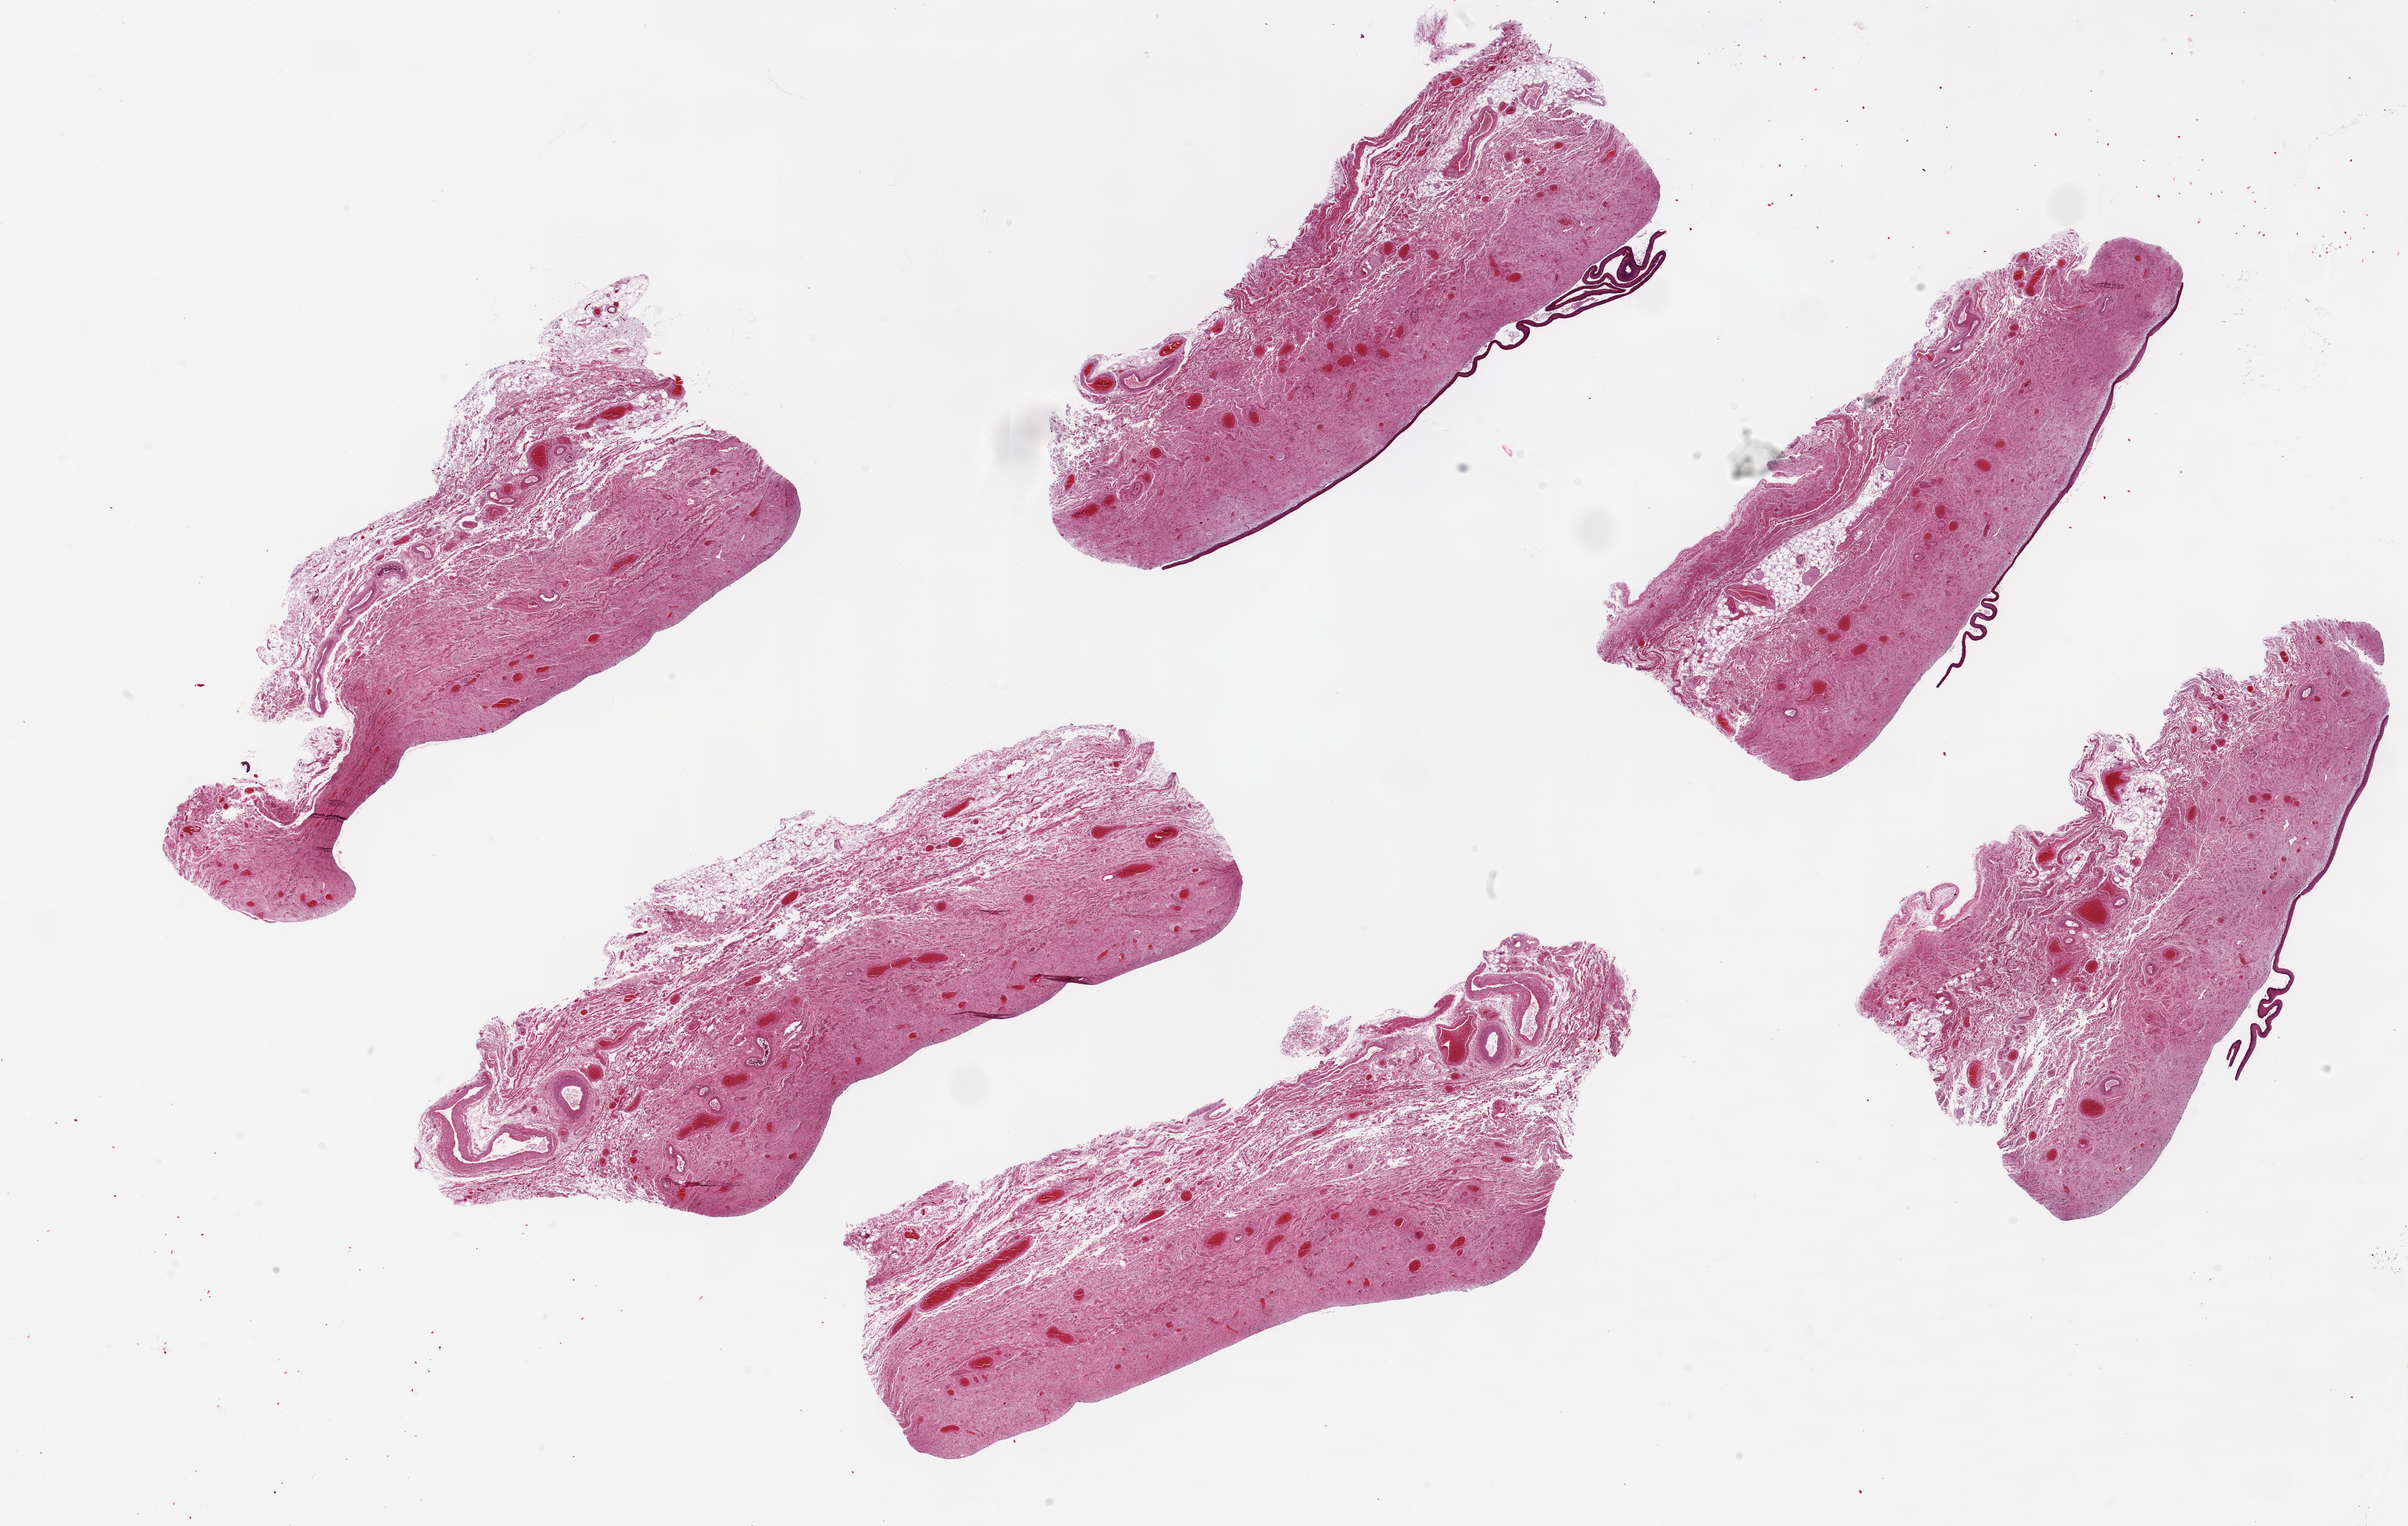
Digitized haematoxylin and eosin-stained section, shown as a low-resolution overview of the whole scanned area (about 30.5 x 19.3 mm), PAXgene-fixed, paraffin-embedded tissue, sampled site (target tissue): vagina, donor tissue sample. Donor: female.
* reviewer comment on this tissue sample: 6 ~9x3mm pieces. Squamous mucosa has sloughed from ~50% of tissue; where present, is ~1% of thickness